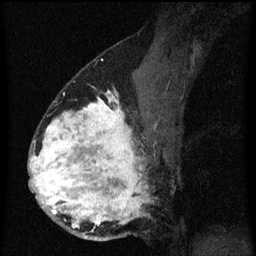
Breast MRI (dynamic contrast-enhanced), one sagittal slice. Slice 39 of 60 in the series (ordered by position). Dynamic contrast-enhanced series, image 2 of 3 at this slice position (ordered by acquisition). 1.5 T. TE 4.2 ms, TR 8.4 ms. 2 mm slice thickness. 256 × 256 image matrix. Female patient, age 34 years. From the clinical record (not read from this slice): setting: breast cancer imaged before/during neoadjuvant chemotherapy; receptor status: HR-positive, HER2-negative.
Annotated regions visible in this slice (semi-automatic segmentation, software-assisted and operator-edited):
- analysis volume of interest (the breast-tissue region the enhancement analysis was run in; not a lesion): bounding box <30,64,165,241> (left, top, right, bottom; pixels)
- tumour enhancement mask (voxels above the 70 % enhancement threshold inside the analysis volume of interest): <30,92,149,229>